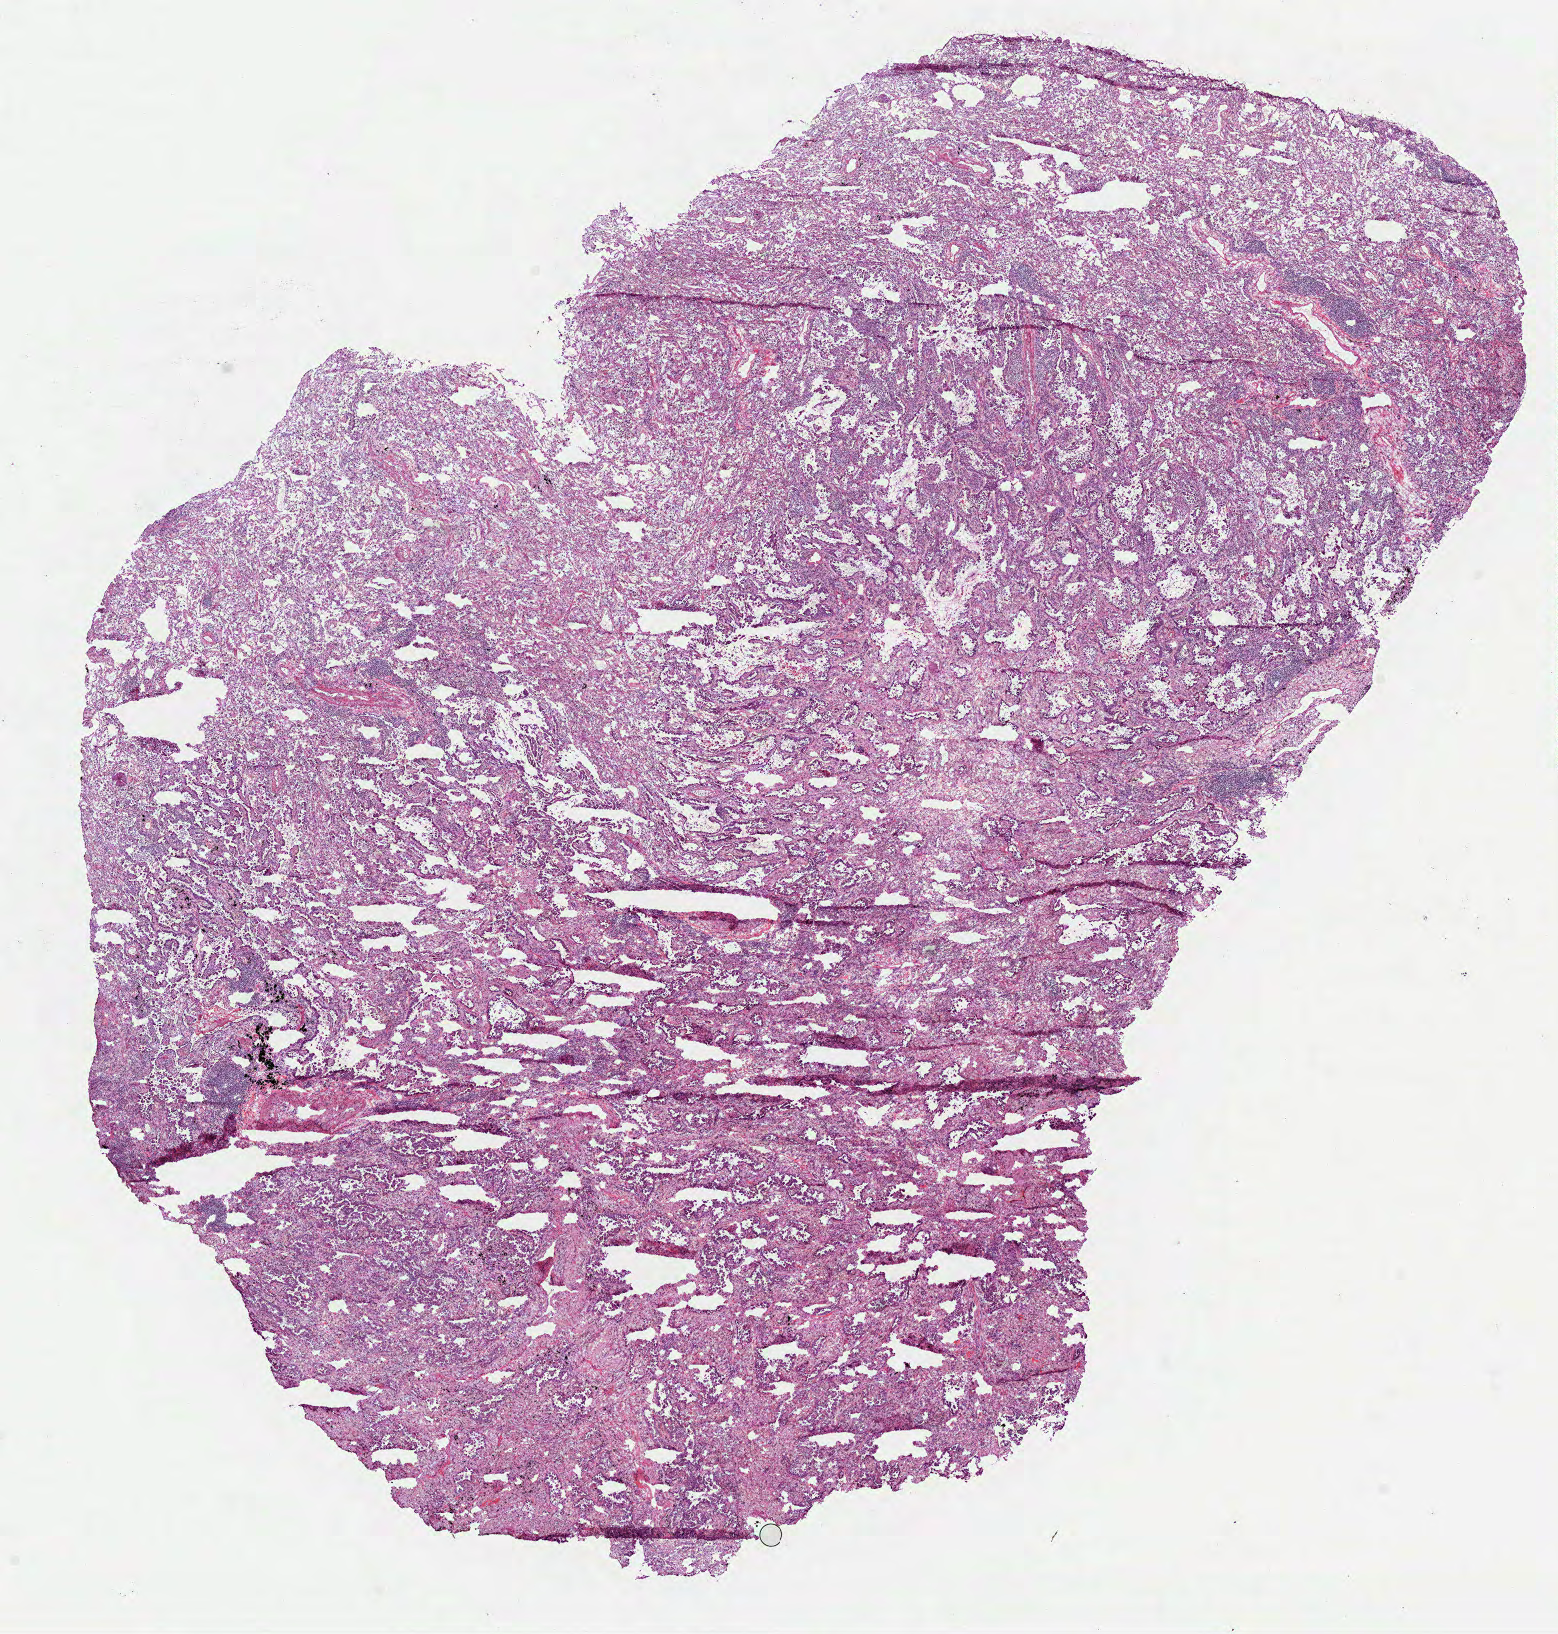
Digitized Hematoxylin and eosin (H&E) stained tissue section (whole slide), low-resolution overview of the scanned area, about 12.6 x 13.2 mm (slide scanned at 40x), frozen section, sample: primary tumour, lung. Patient: female, age at initial diagnosis 83 years. Pathologist review of this section (percent, as recorded): tumour cells 95%, tumour nuclei 55%, normal cells 5%, necrosis 0%. Infiltration values recorded for this section: lymphocyte infiltration 15%, monocyte infiltration 5%.
Pathologic diagnosis: Papillary adenocarcinoma, NOS (lower lobe, lung). Laterality: left. AJCC pathologic stage: IIIA.